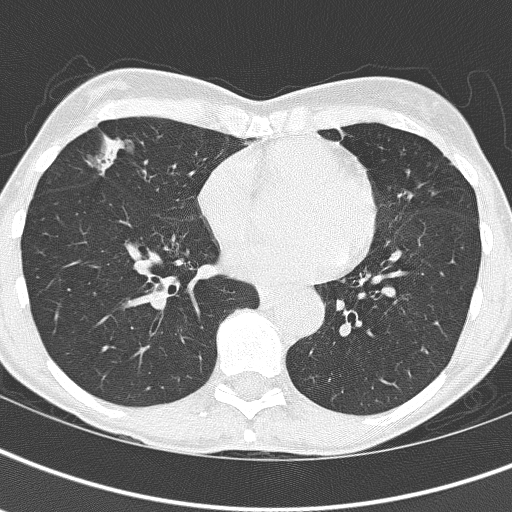
Axial slice from a low-dose chest CT screening exam, baseline annual screen, lung window (W 1500 / L -600 HU), 2 mm slice thickness, 120 kVp. Female, age 67 years at enrolment. Current smoker at enrolment.
- Lesion marked by an expert reader, bounding box <85,124,178,206> (left, top, right, bottom; pixels).
- No non-calcified nodule or mass ≥4 mm was recorded by the screening reader at this exam.
- Official screen result: negative screen, significant abnormalities not suspicious for lung cancer.
- Lung cancer was diagnosed 832 days after this screen: bronchiolo-alveolar adenocarcinoma, NOS, right middle lobe, well differentiated (G1), stage IA (AJCC 6th edition), 25 mm at pathology.